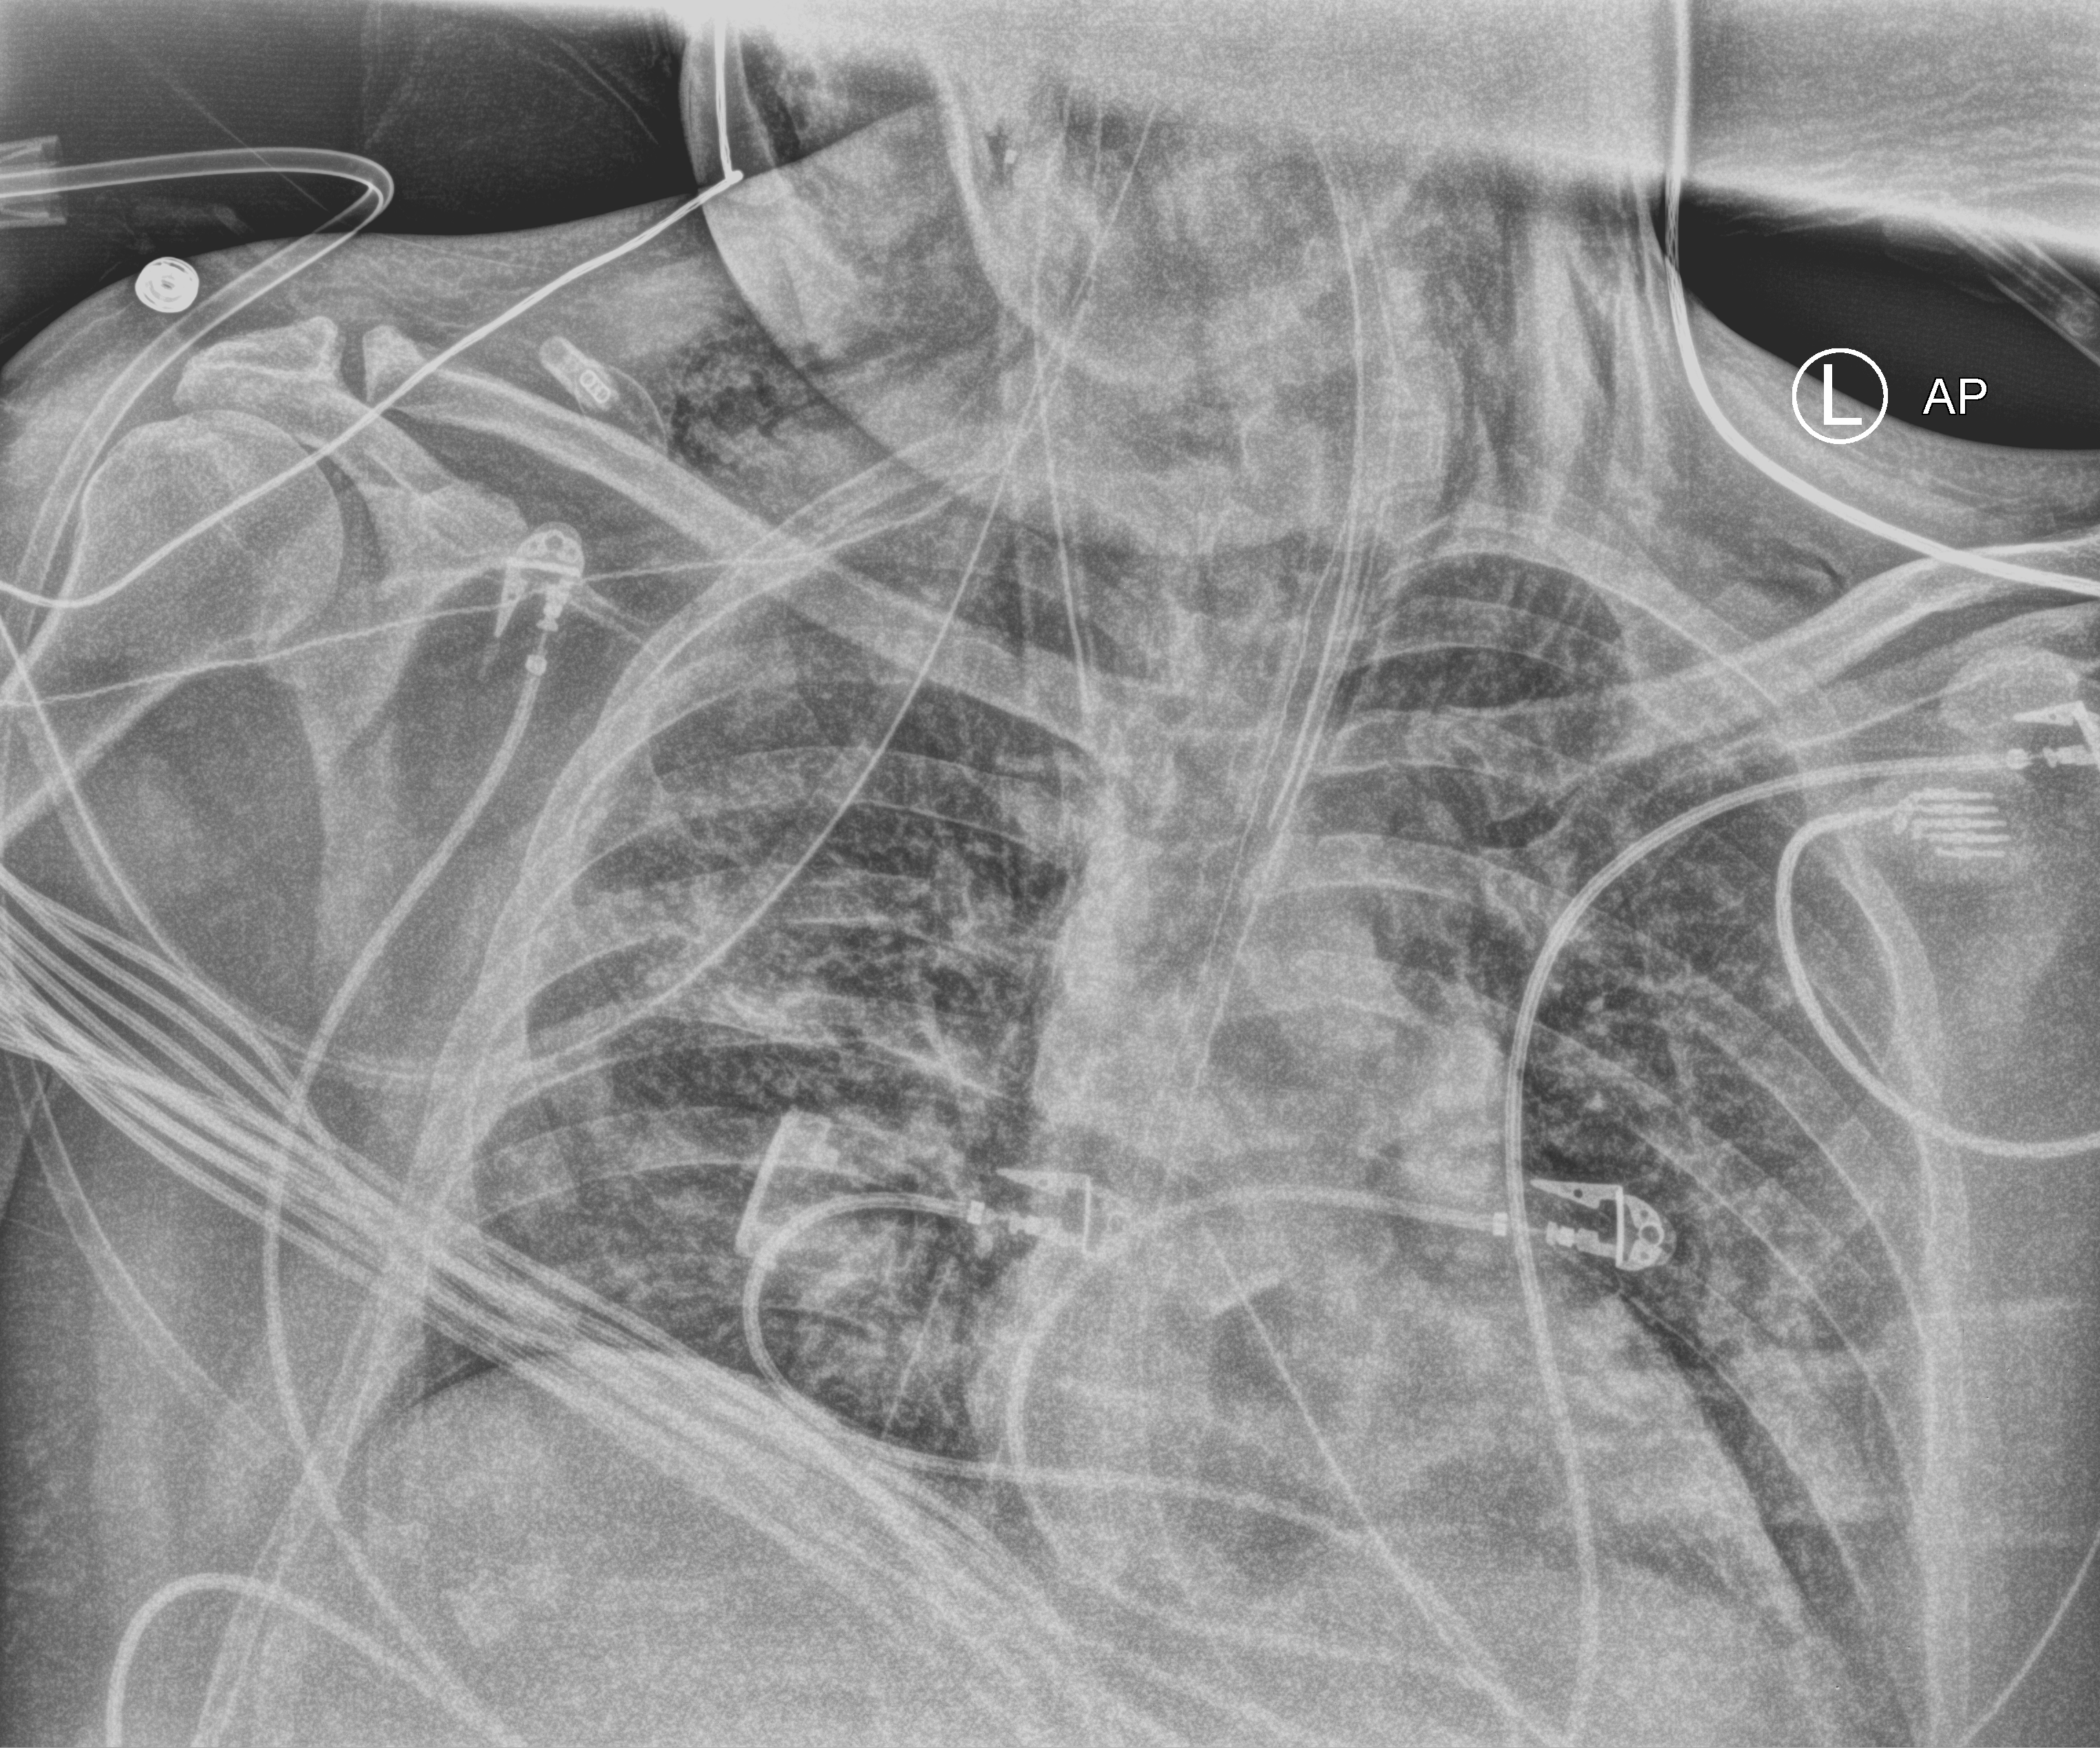
Bedside chest radiograph (computed radiography); anteroposterior (AP) projection. Adult patient hospitalised with COVID-19, age 18–59 years.
Hospital-stay facts (about this admission, not read from this image; timing relative to this image not recorded):
- mechanically ventilated during this hospital stay: yes
- COPD (admission record): no